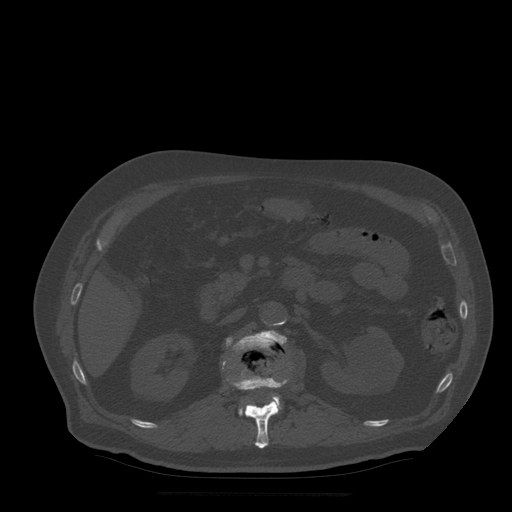
CT including the spine, one axial slice. Bone window (W 1800 / L 400 HU). 1.25 mm slice thickness. 512 × 512 image matrix. Patient age 72 years. From the clinical record (not read from this slice): primary cancer: prostate.
Annotated regions visible in this slice (semi-automatic segmentation, software-assisted and operator-edited):
- L1 vertebra: box from (x=227, y=372) to (x=288, y=449) px
- L2 vertebra: (x=227, y=331)–(x=288, y=416)